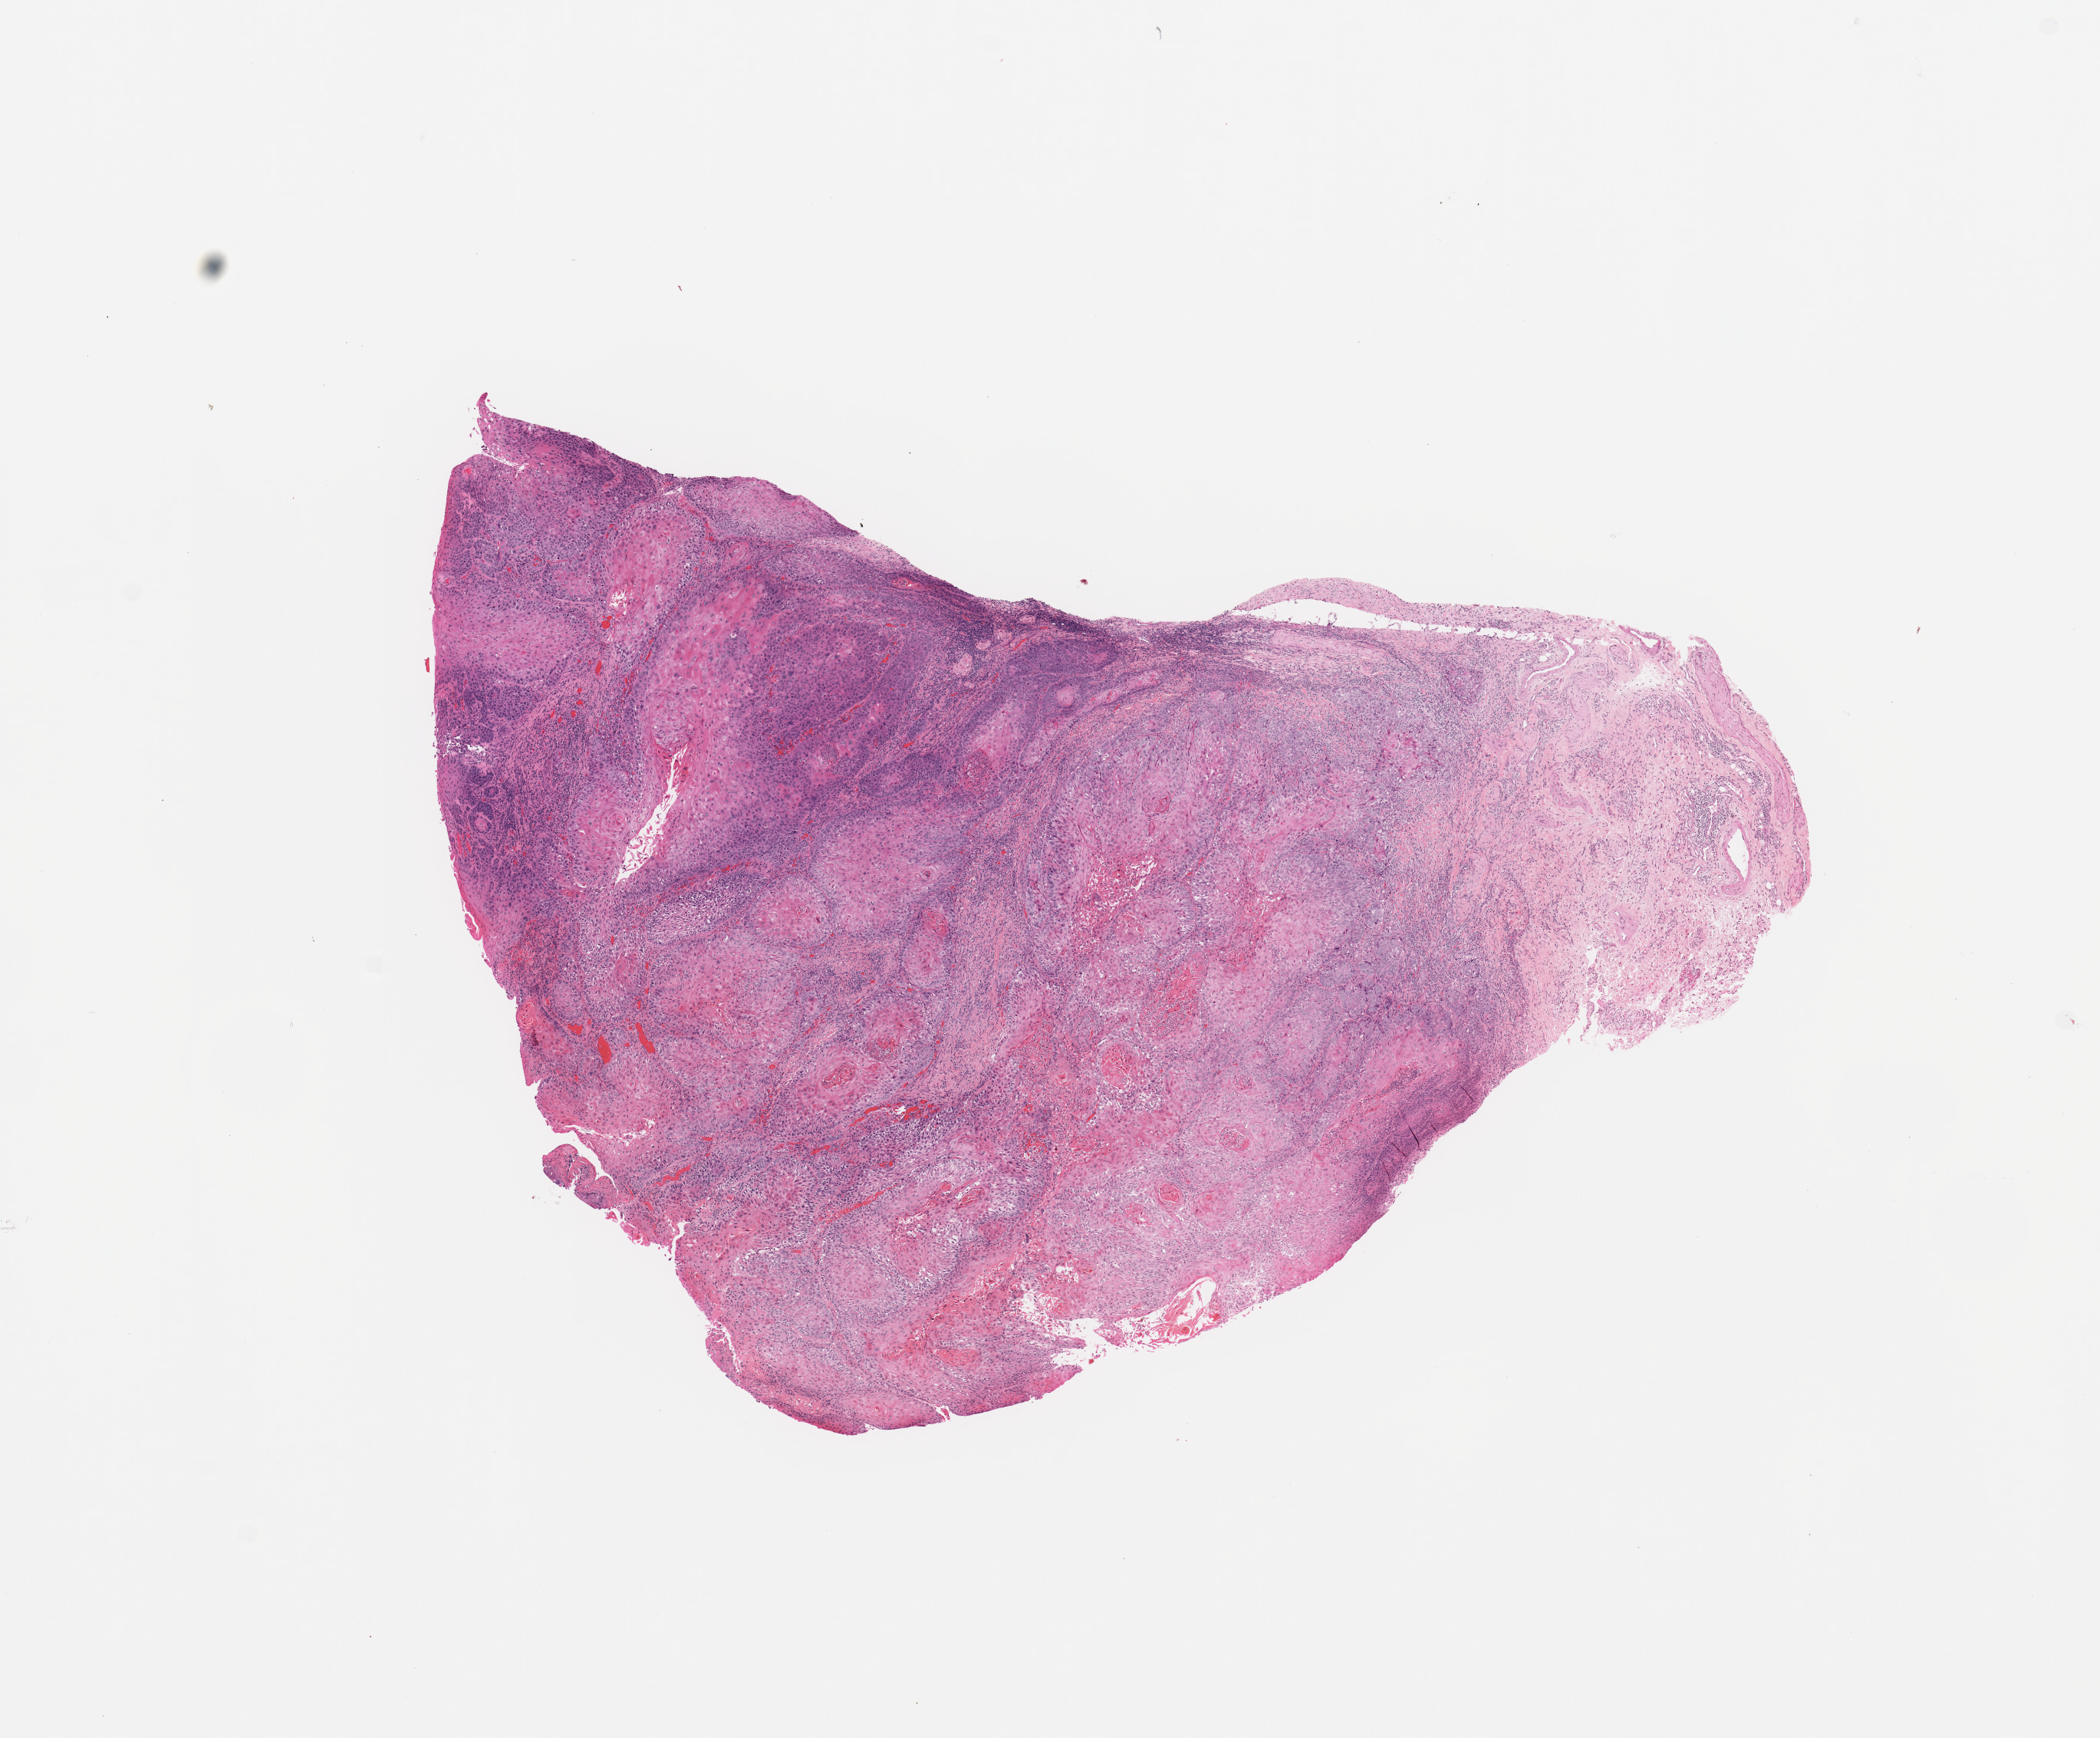
Whole-slide histology image, H&E — a low-resolution overview of the entire scanned area, about 10.8 x 9.0 mm. Tumour tissue sample, sampled site: oral cavity. Patient: male, age 56 years. Histologic grade: G1 (well differentiated). Composition of this section per pathologist review: tumour nuclei 80%, necrosis 3%.
• histologic diagnosis: Squamous cell carcinoma, NOS (overlapping lesion of lip, oral cavity and pharynx)
• primary tumour site (as recorded): oral cavity
• AJCC pathologic stage: III